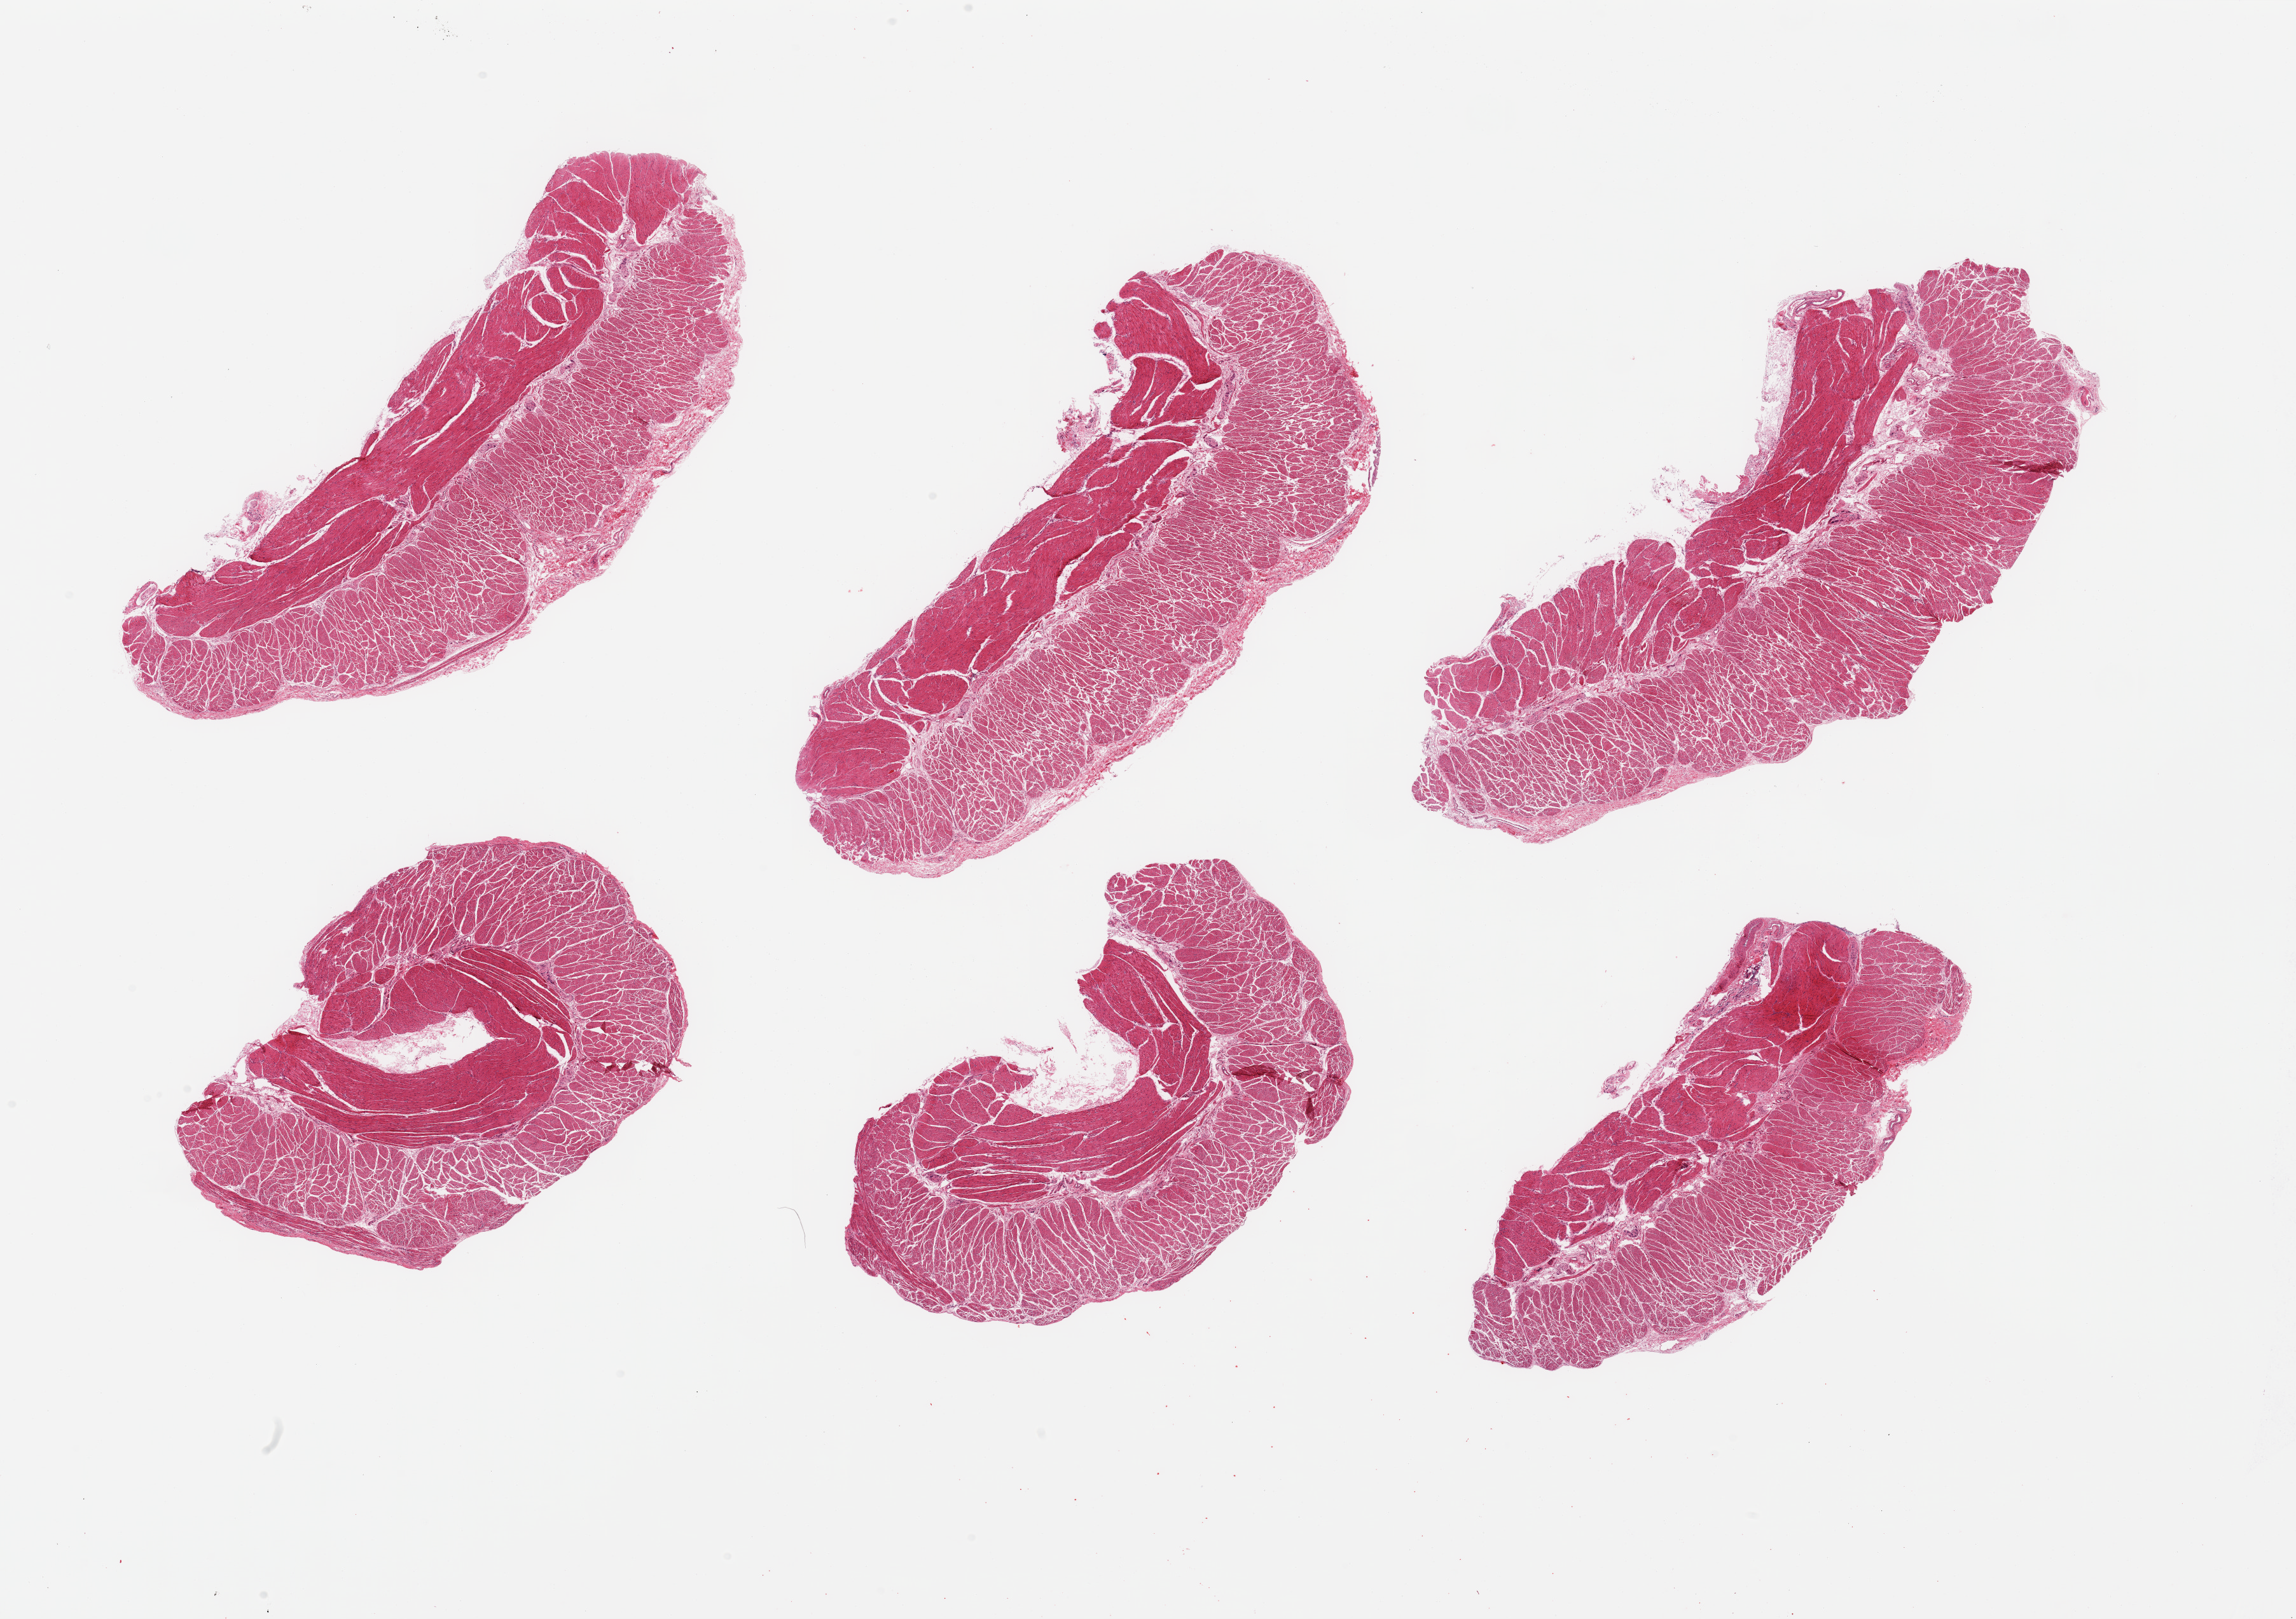
Haematoxylin and eosin whole-slide image, a low-resolution overview of the entire scanned area, about 28.5 x 20.1 mm. PAXgene-fixed paraffin-embedded (PFPE) section. Target tissue: esophageal muscle. Donor tissue sample.
Pathologist's review note for this sample: 6 pieces; target muscularis.